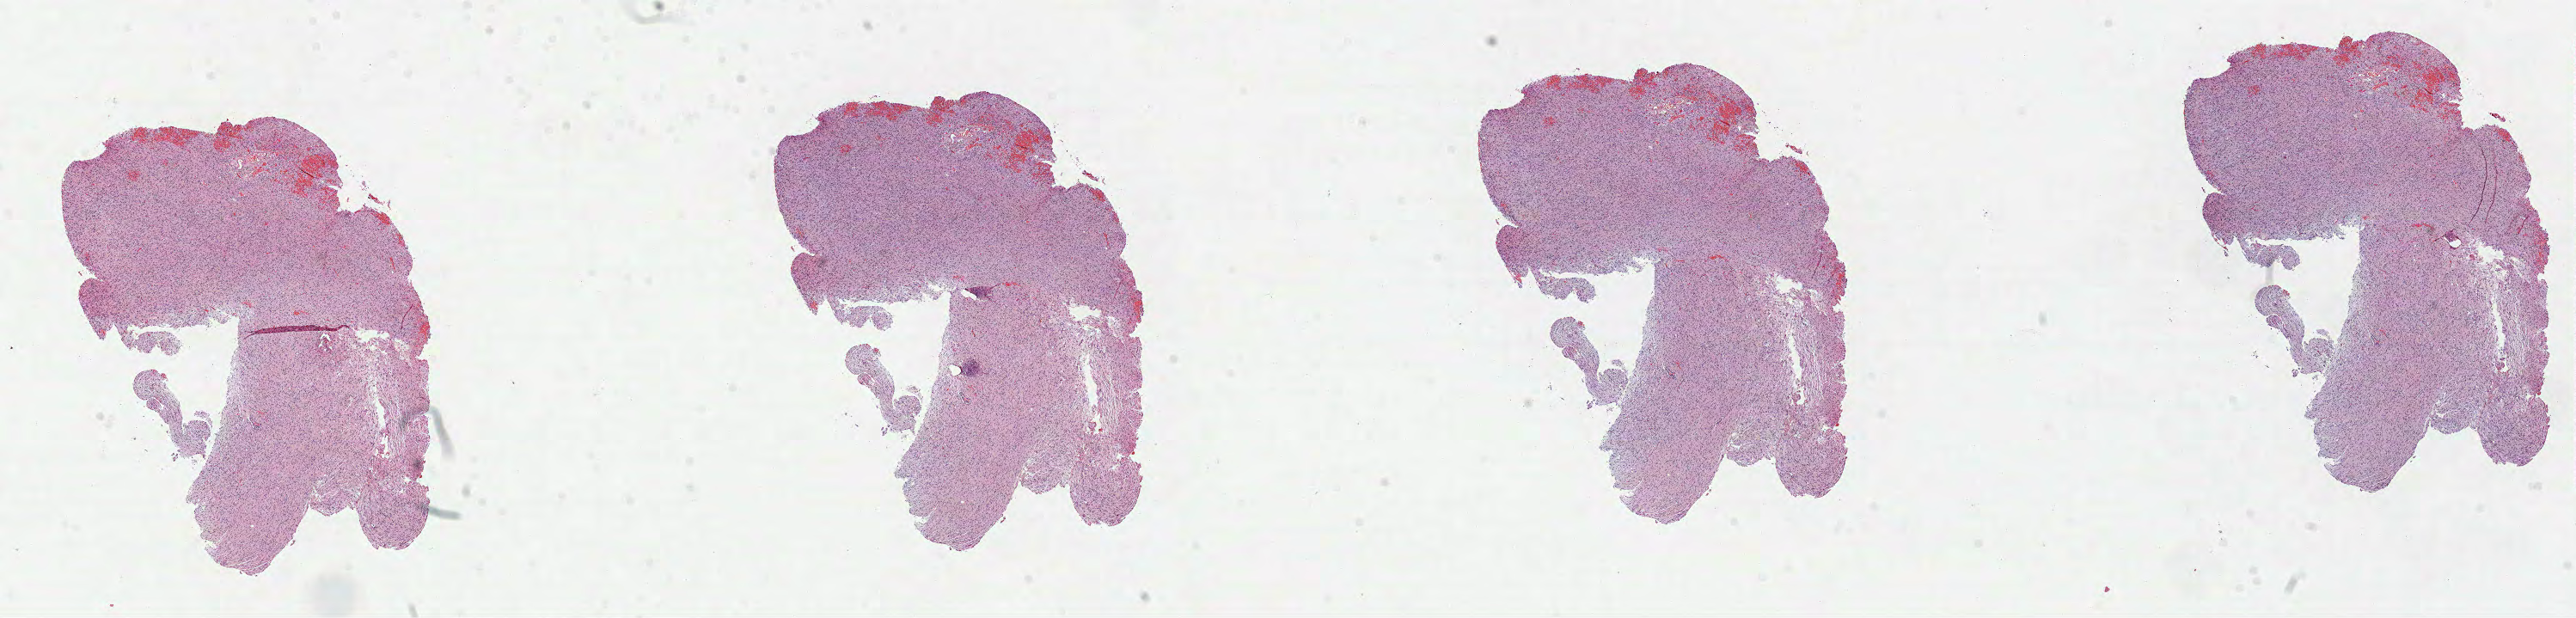
Whole-slide histology image, Hematoxylin and eosin (H&E) stained — shown as a low-resolution overview of the whole scanned area (about 24.2 x 5.8 mm, from a 40x scan); FFPE section; primary tumour sample from the brain. Female, age 57 years at initial diagnosis.
Diagnosis: Astrocytoma, anaplastic.